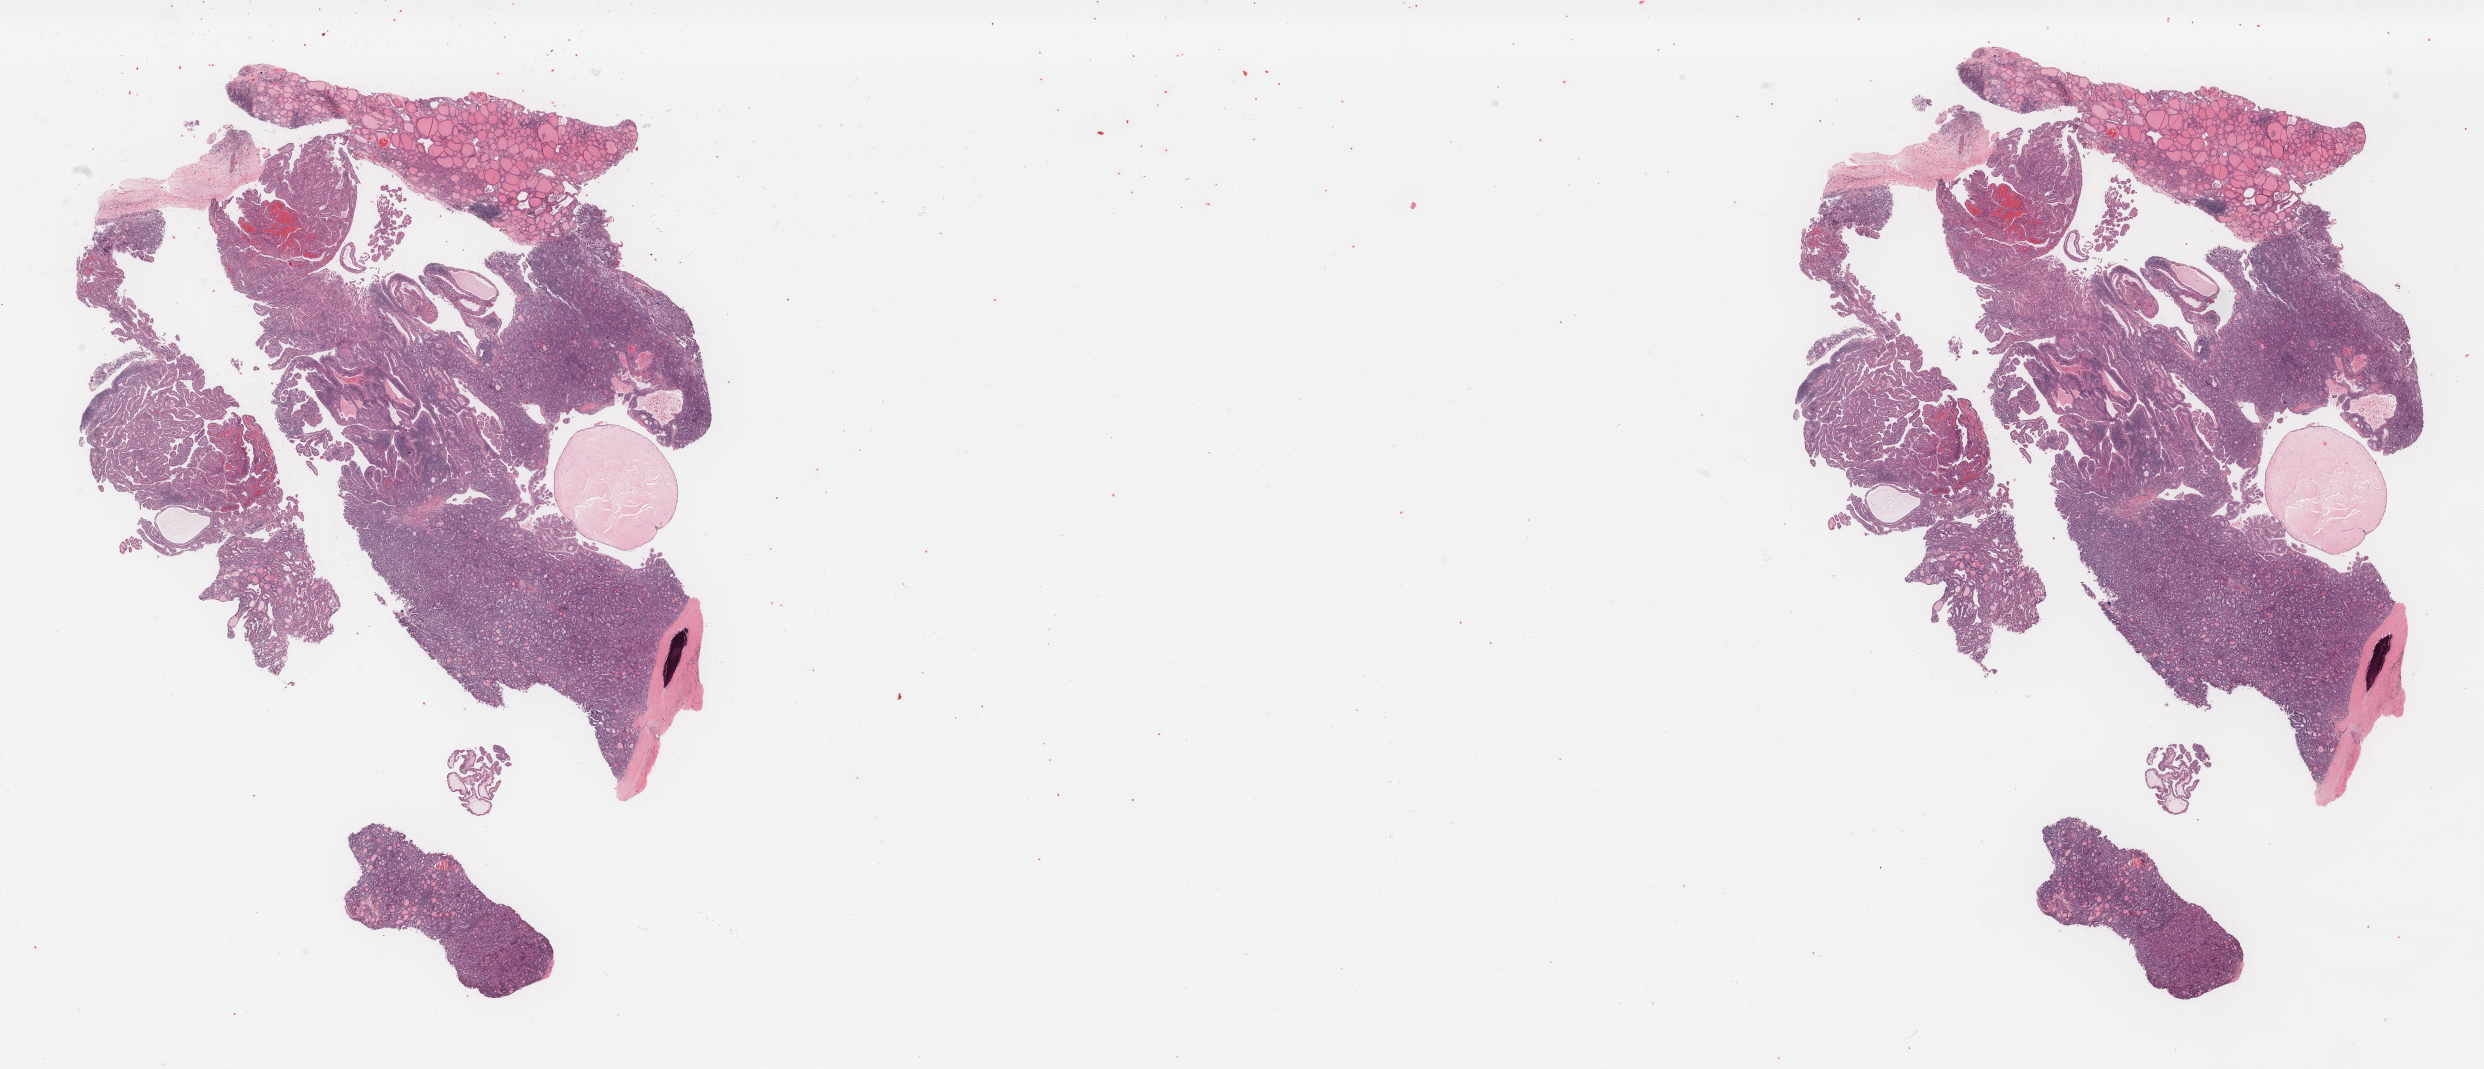
Whole-slide histology image, H&E-stained — whole scanned area (about 39.3 x 16.9 mm, slide scanned at 40x) shown as a low-resolution overview. FFPE section. Thyroid, primary tumour sample. Female patient; age at initial diagnosis 61 years.
Histologic diagnosis: Papillary adenocarcinoma, NOS (thyroid gland). Lymph nodes positive (case pathology): 1 of 4 examined. AJCC pathologic stage: III (7th edition).